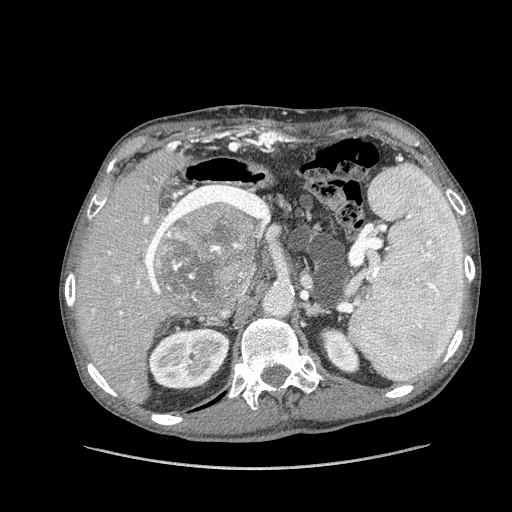
Contrast-enhanced abdominal CT (liver protocol), one axial slice. Position 81 of 162 along the scan axis. 100 kVp. Soft-tissue window (W 400 / L 40 HU). 512 × 512 image matrix, field of view 400 × 400 mm. From the clinical record (not read from this slice): diagnosis: hepatocellular carcinoma (patient treated with transarterial chemoembolisation; whether this scan precedes or follows treatment is not stated here); TNM stage (as recorded): Stage-IIIA; Child-Pugh class: A; tumour nodularity: multinodular; tumour size: 9.9 cm.
Structures marked on this image (semi-automatic segmentation, software-assisted and operator-edited):
- liver parenchyma outside the tumour (the mass and vessels are separate outlines, so this box may not span the whole liver): bounding box <76,147,266,402> (left, top, right, bottom; pixels)
- mass: <154,201,258,309>
- liver vessels: <92,204,265,349>